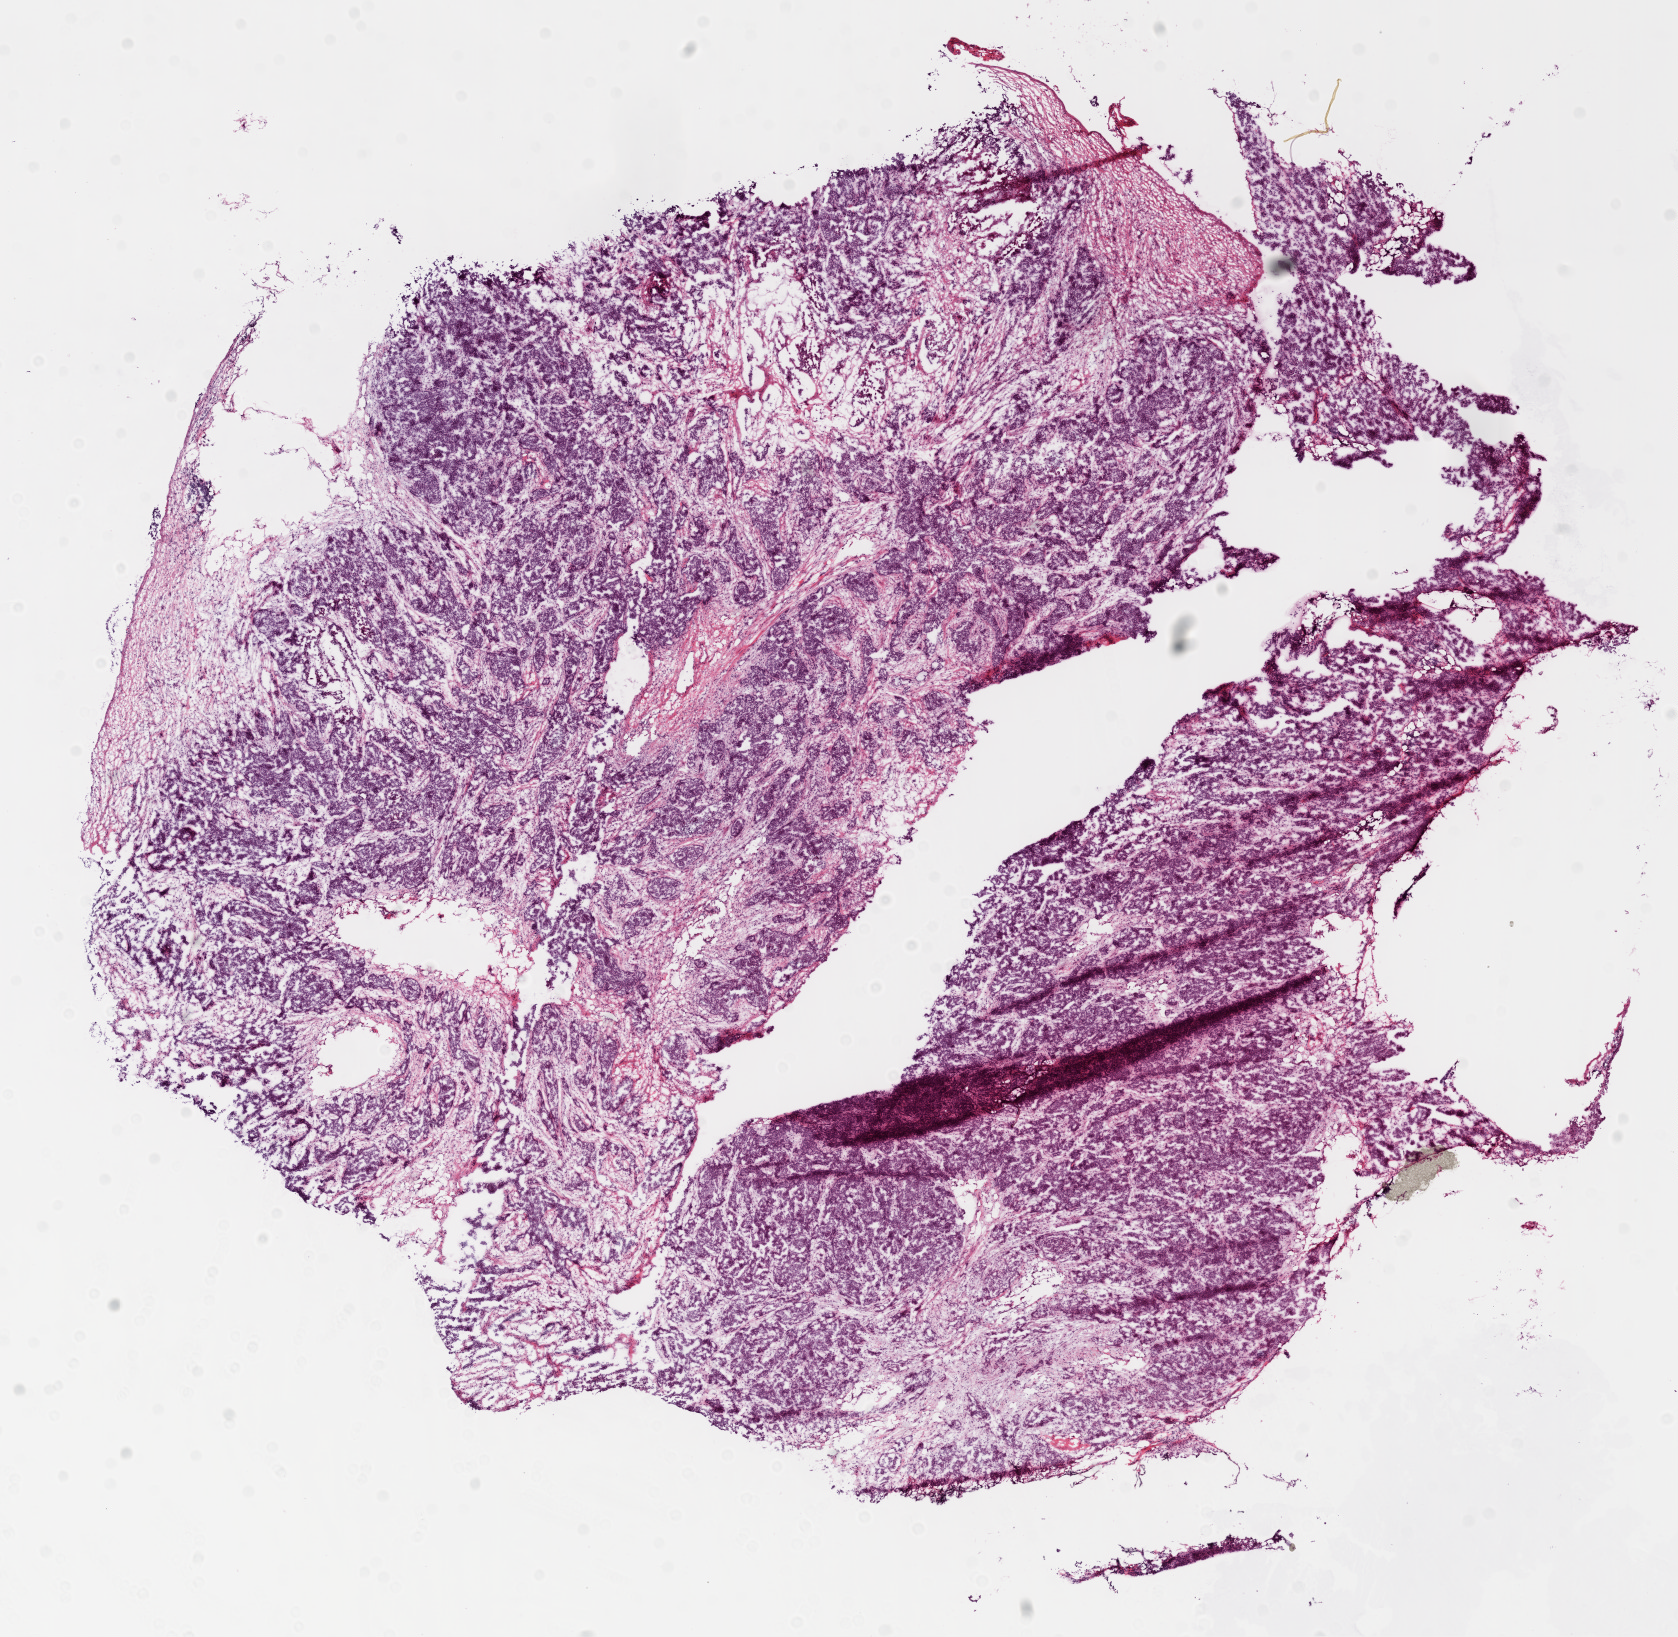
Whole-slide histology image, H&E — a low-resolution overview of the entire scanned area, about 13.5 x 13.2 mm, frozen section from the top of the tissue portion, ovary, primary tumour sample. Patient: female, age at initial diagnosis 55 years. Histologic grade: G3 (poorly differentiated). Slide review estimates, as recorded: tumour cells 80%, tumour nuclei 81%, normal cells 19%, necrosis 1%.
- FIGO stage: IV
- diagnosis: Serous cystadenocarcinoma, NOS